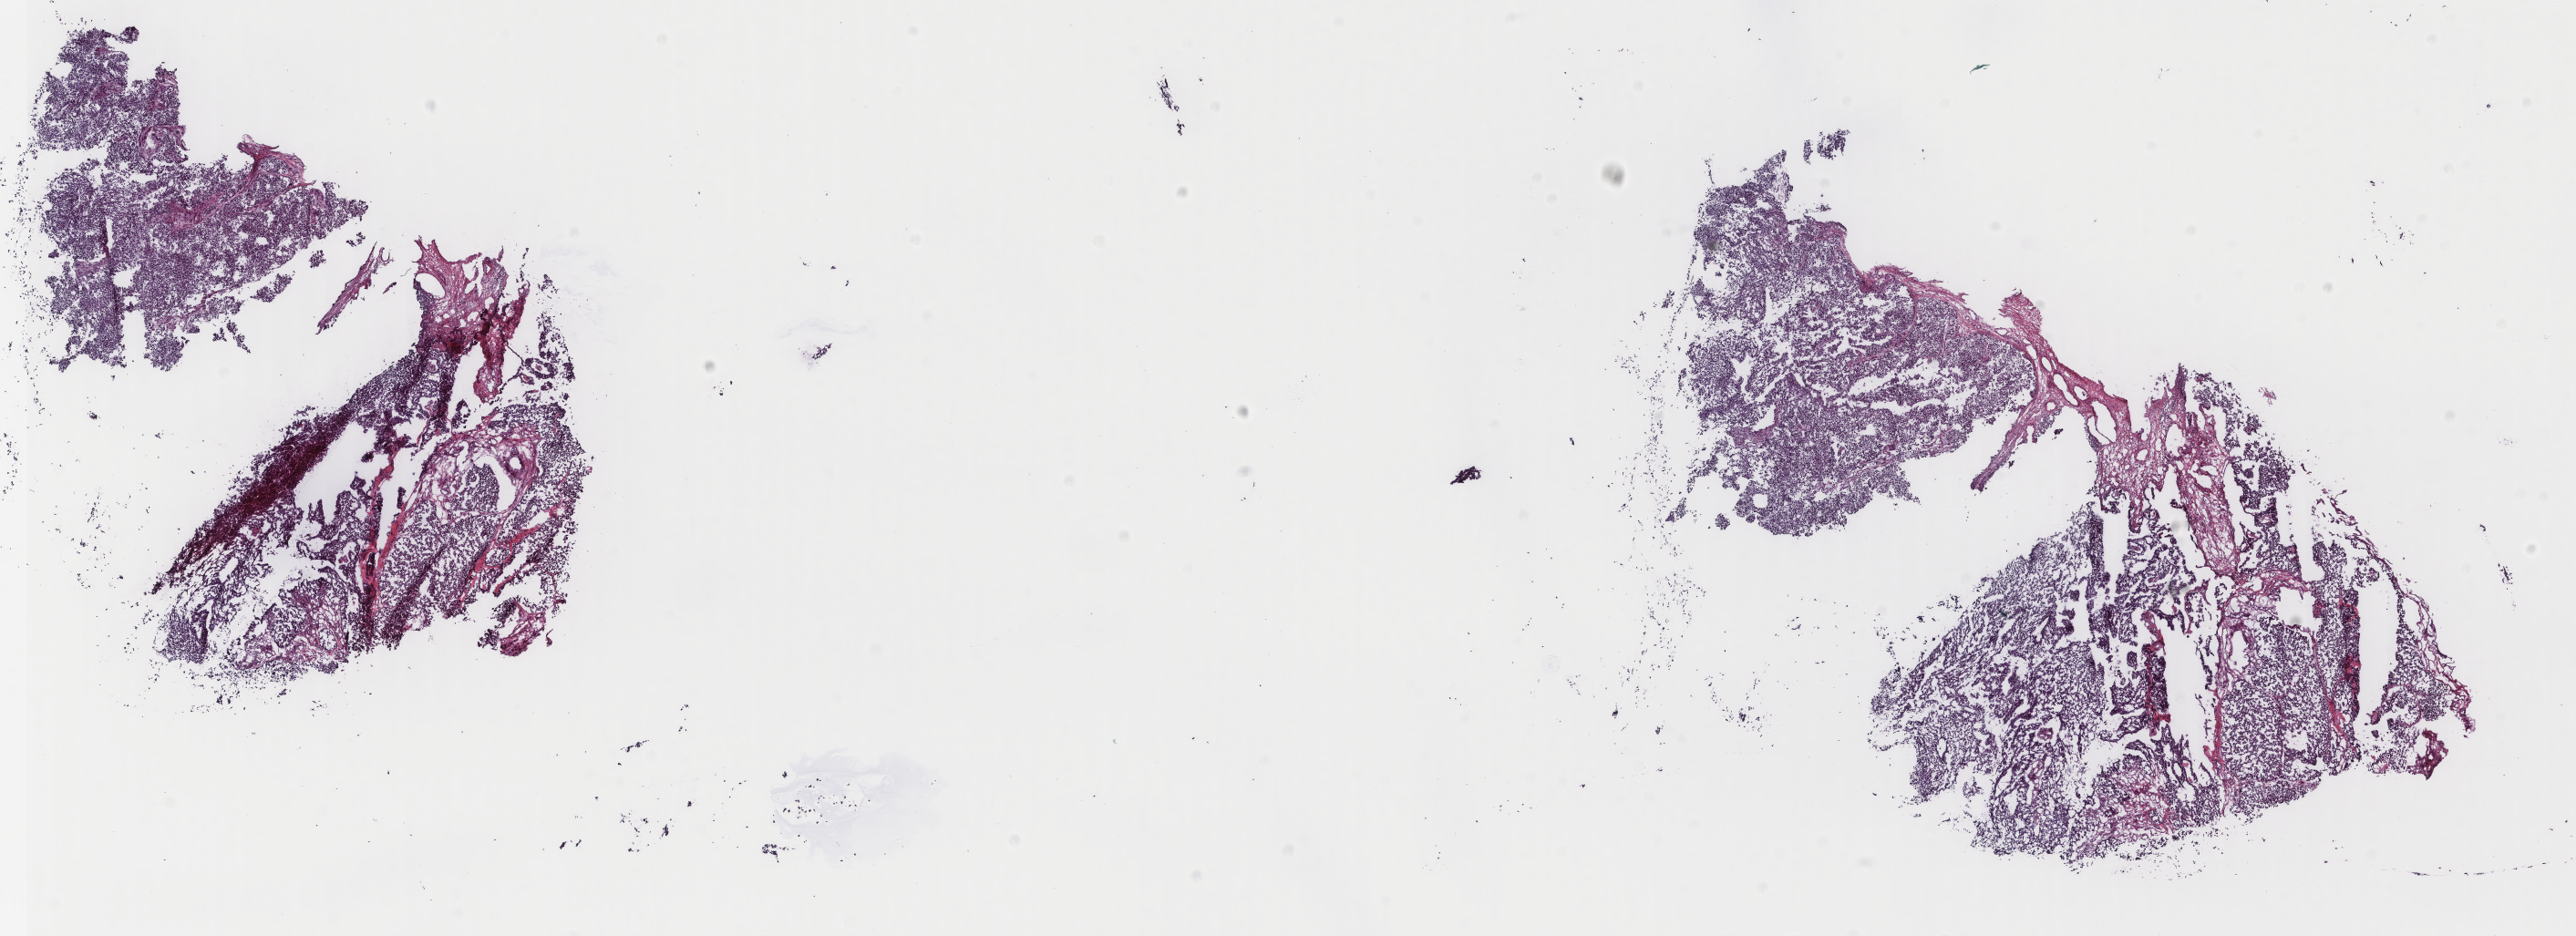
Whole-slide histology image, Hematoxylin and eosin (H&E) stained — shown as a low-resolution overview of the whole scanned area (about 22.4 x 8.2 mm, slide scanned at 40x), frozen section from the top of the tissue portion, primary tumour sample from the bladder. Male, age 68 years at initial diagnosis.
Pathologic diagnosis: Transitional cell carcinoma.